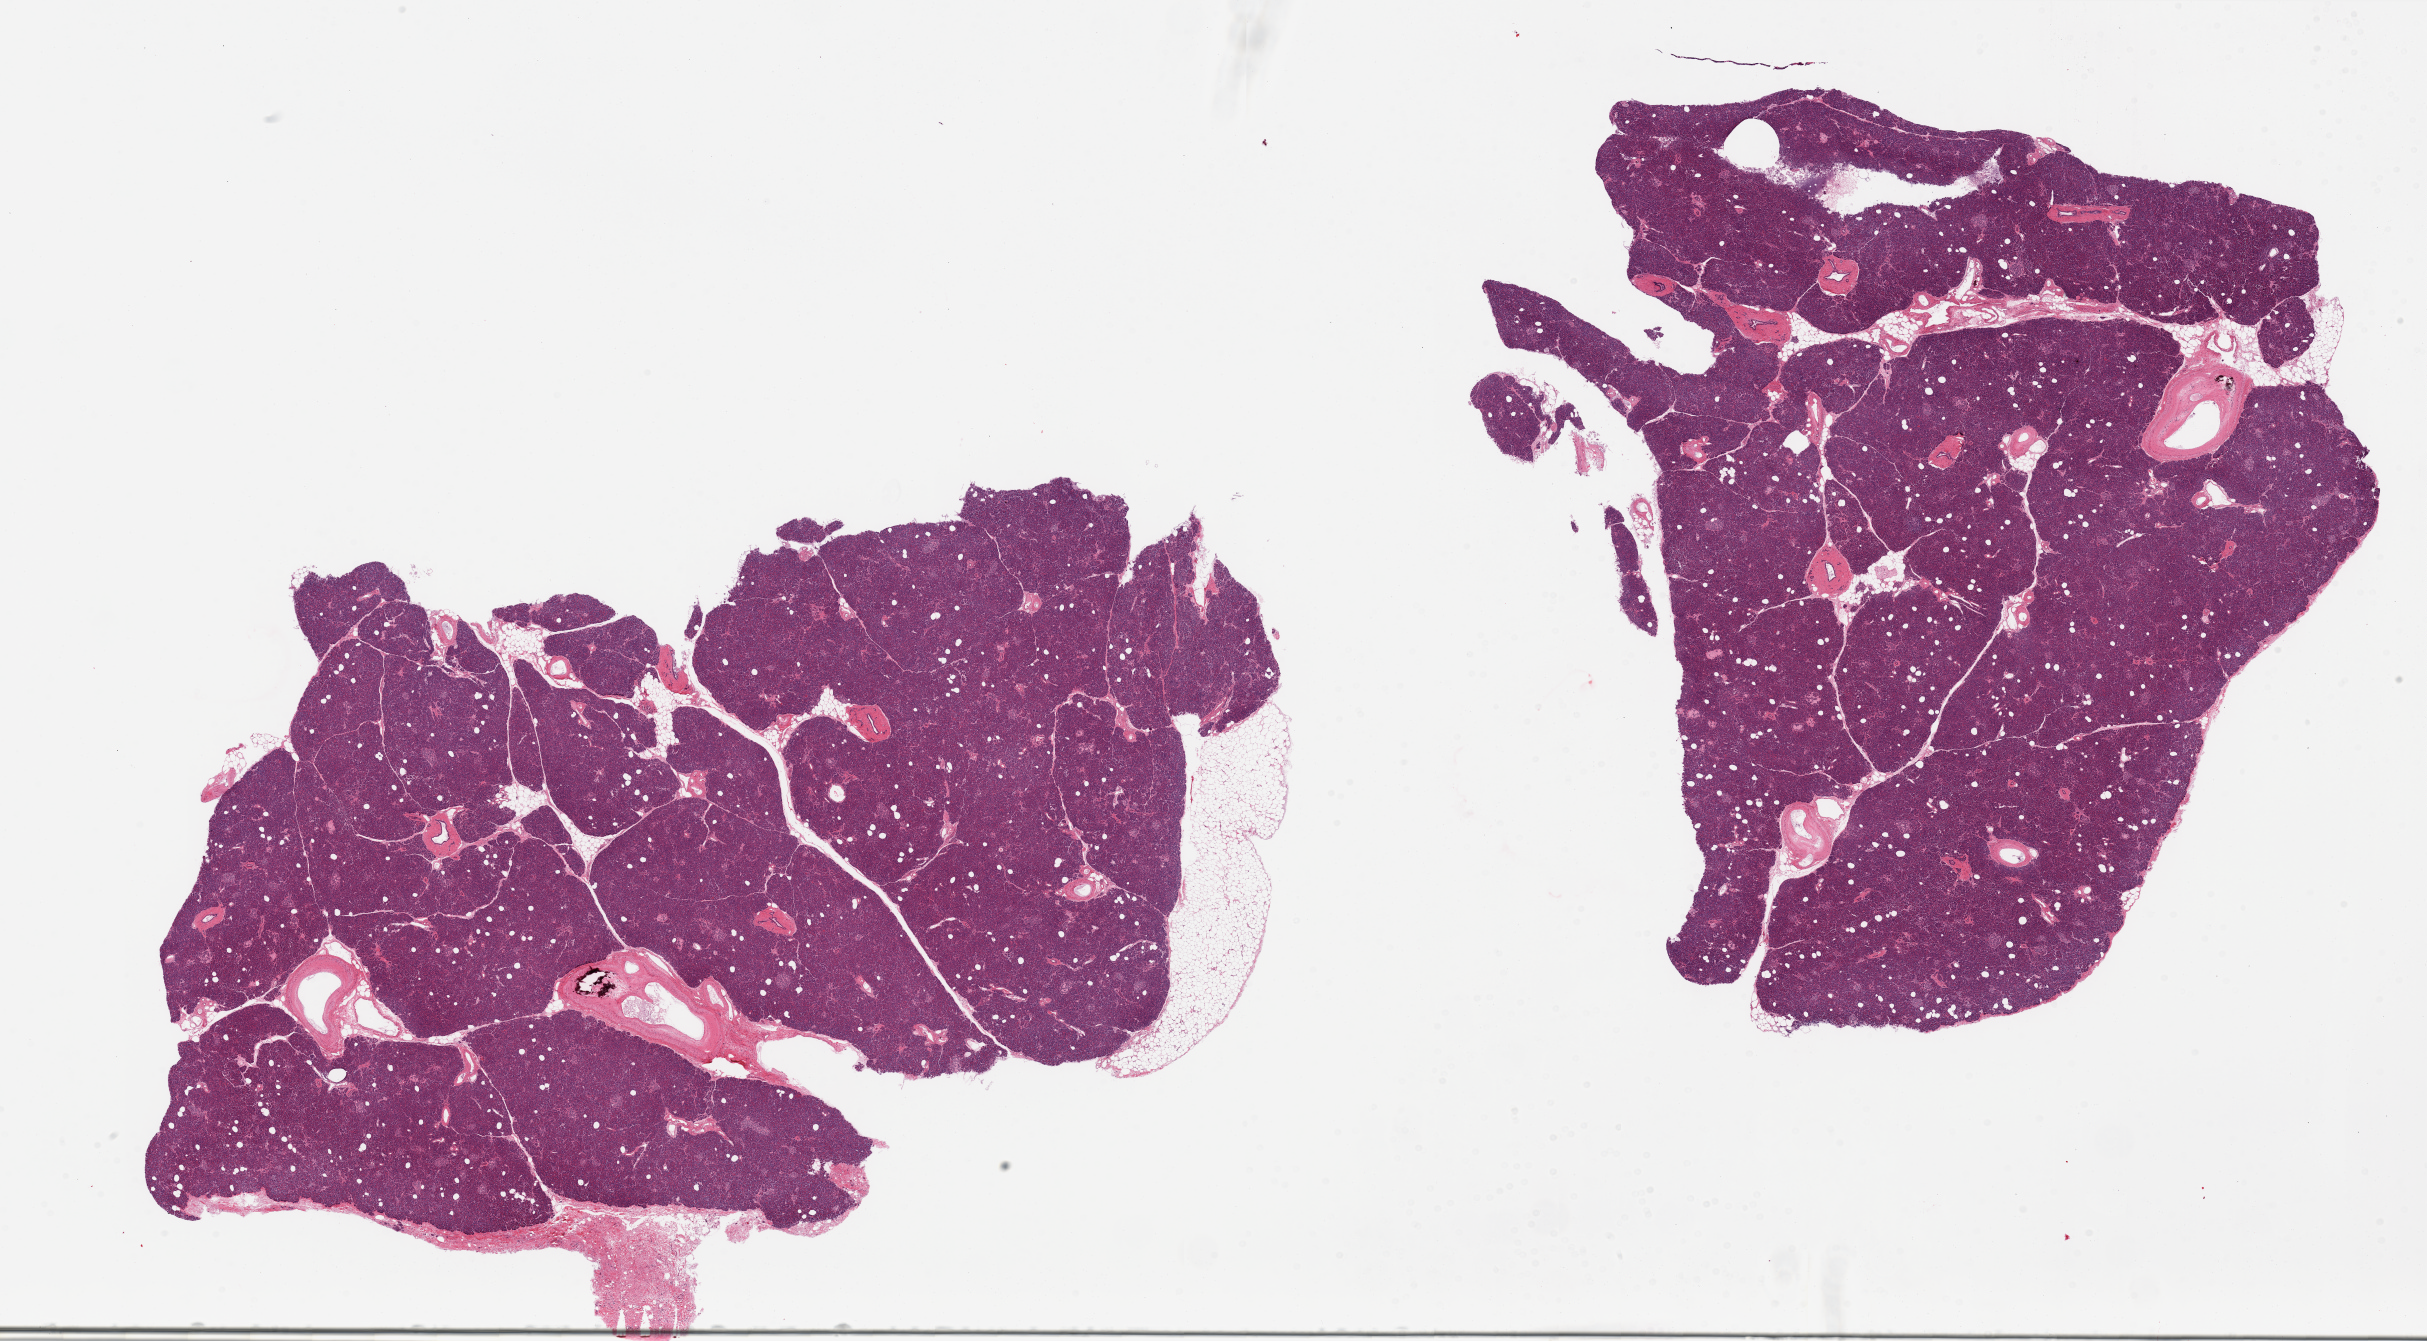
Whole-slide image, hematoxylin and eosin (H&E) stain, brightfield, shown as a low-resolution overview of the whole scanned area (about 38.4 x 21.2 mm); PAXgene-fixed paraffin-embedded (PFPE) section; target tissue: pancreas; tissue donor sample. Donor sex: male.
Review note (as recorded): 2 pieces, 1 with 10% external fat.